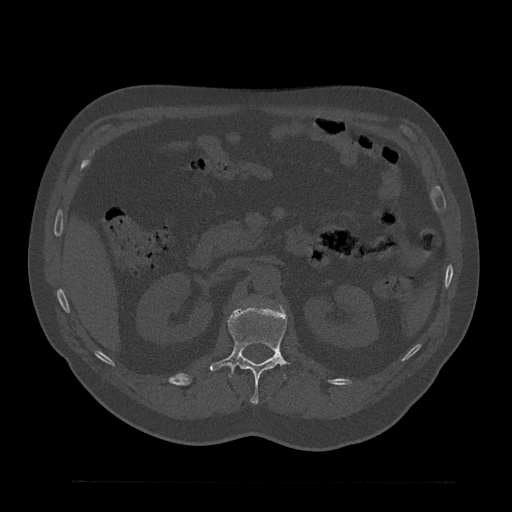
CT including the spine, one axial slice; position 161 of 797 along the scan axis; bone window (W 1800 / L 400 HU); 0.5 mm slice thickness; 512 × 512 image matrix, field of view 430 × 430 mm. Patient: male, 61 years. From the clinical record (not read from this slice): primary cancer: prostate.
Annotated regions visible in this slice (semi-automatically segmented with operator editing):
- L1 vertebra: bounding box [x1, y1, x2, y2] px = [210, 306, 290, 404]